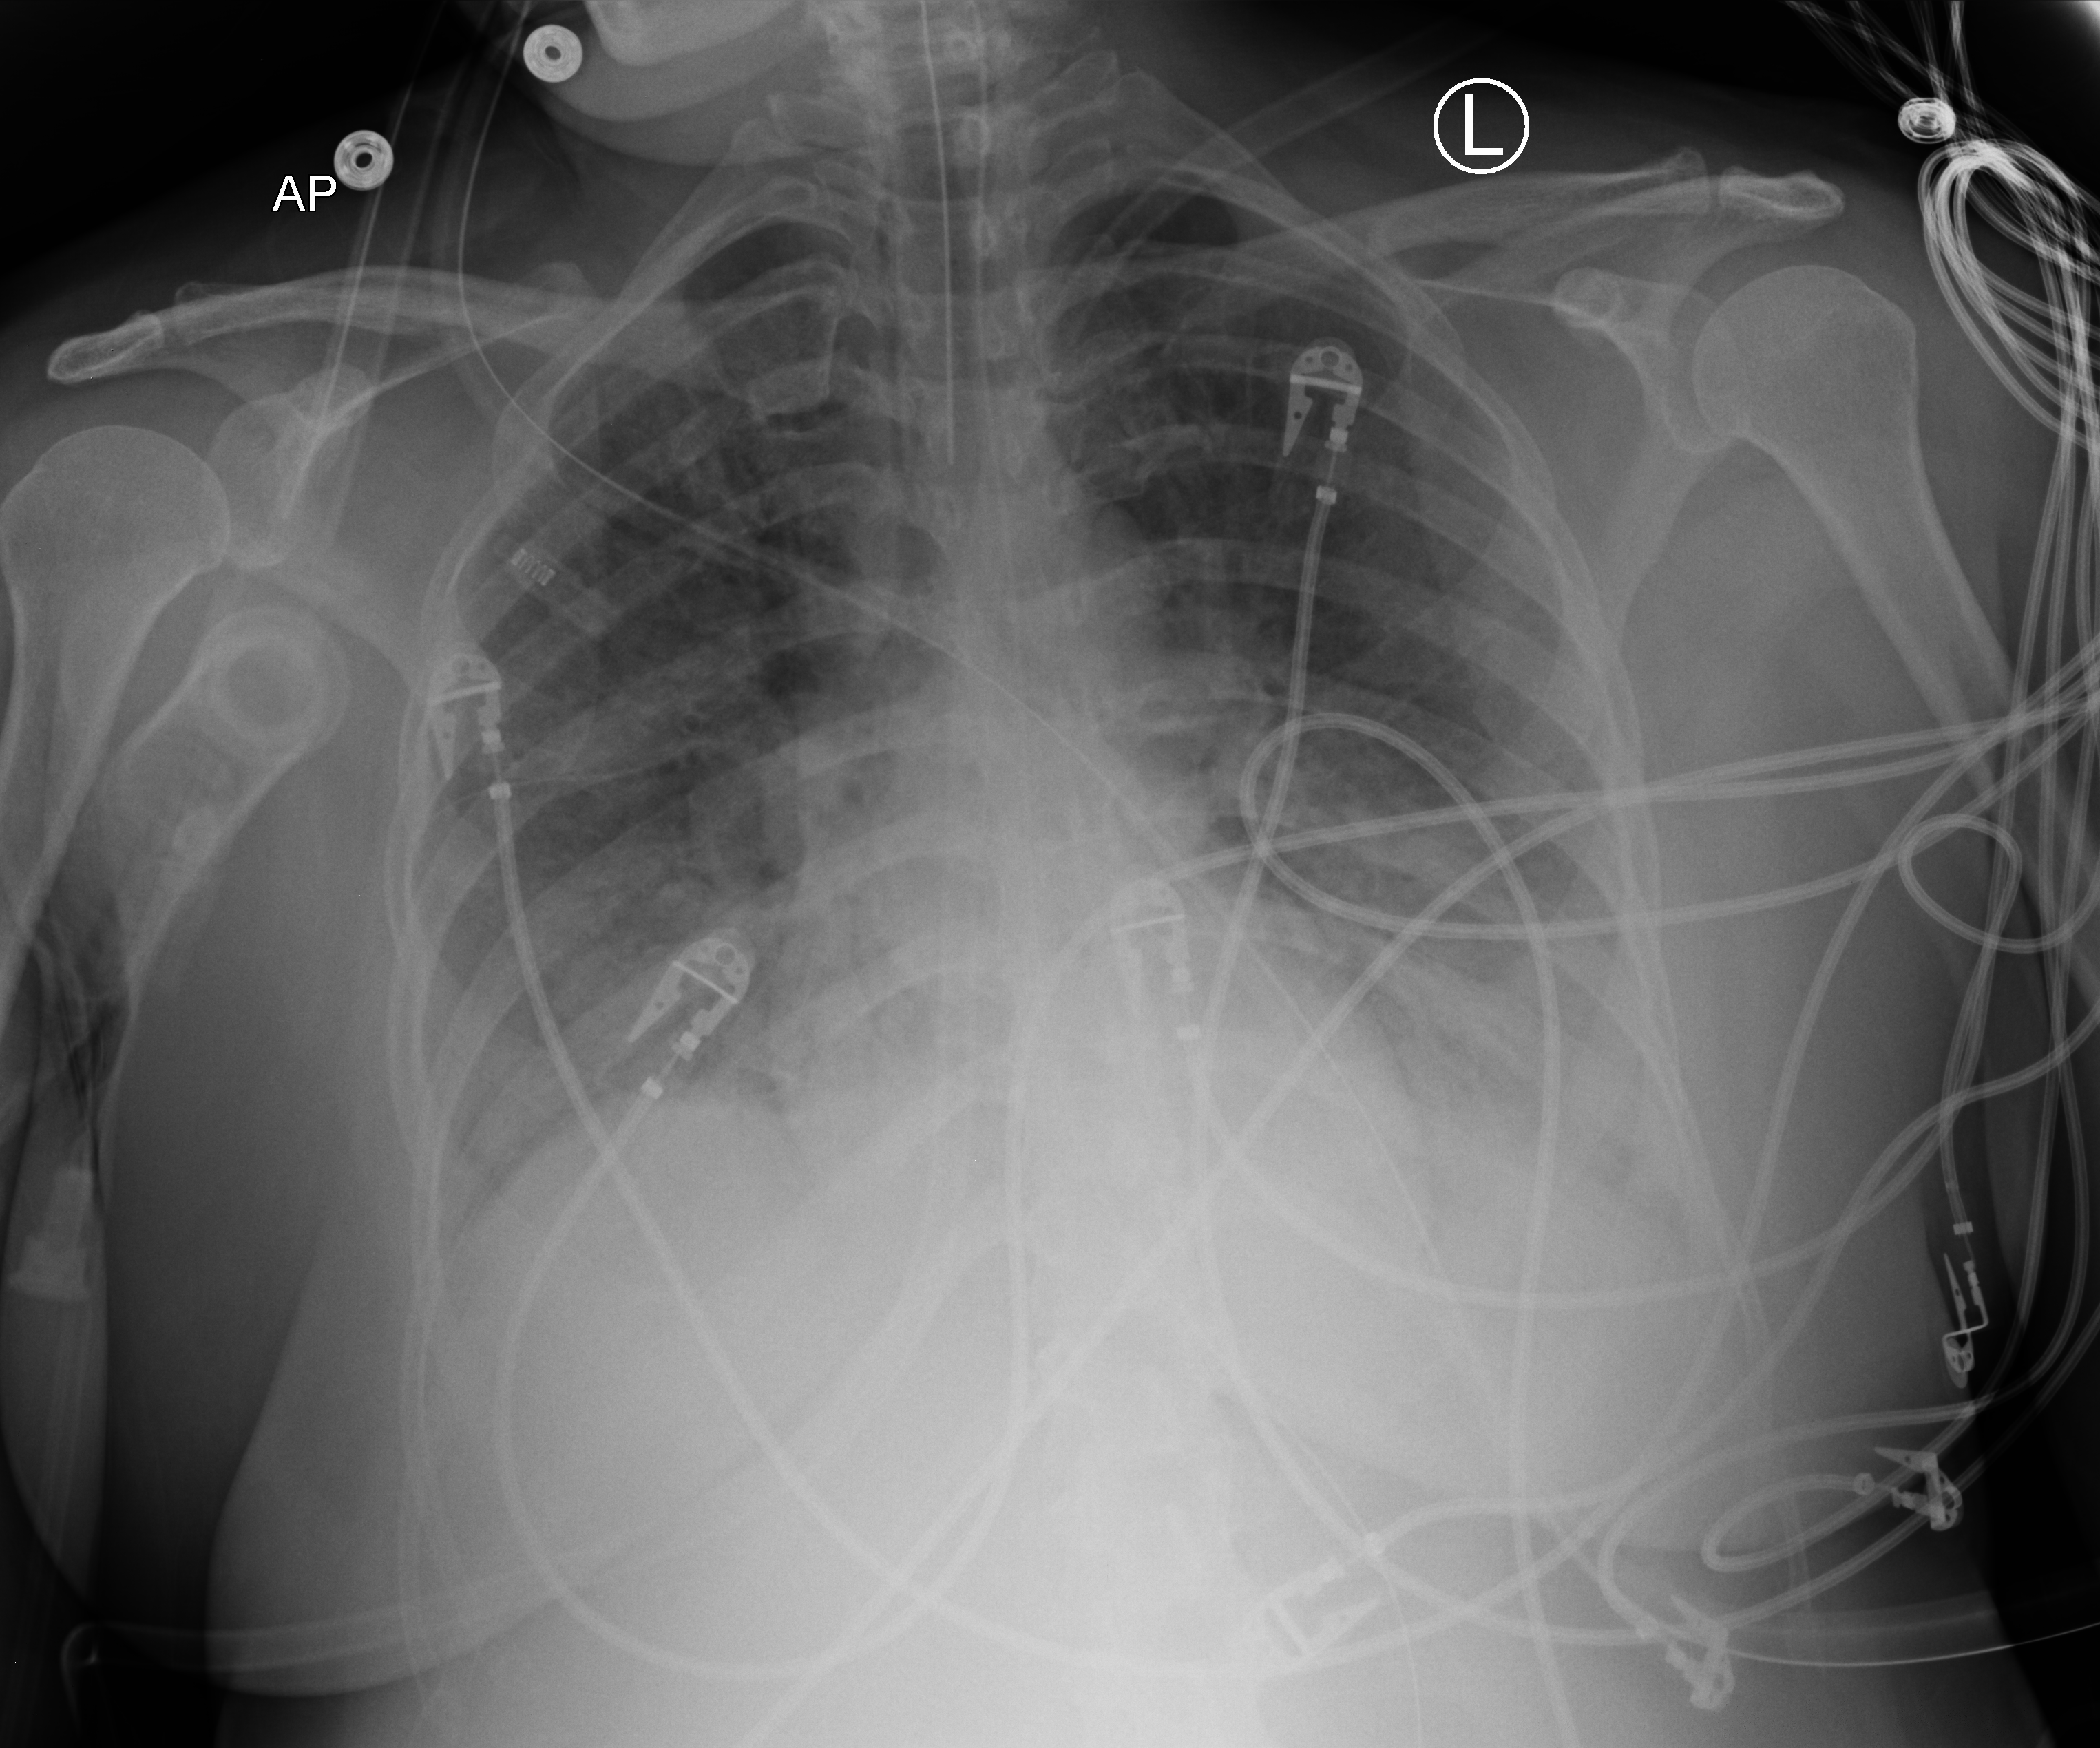
Bedside chest radiograph (computed radiography), anteroposterior (AP) projection. Male patient hospitalised with COVID-19, age 18–59 years.
Admission-level facts for this patient (not findings on this image; timing relative to this image not recorded):
- hypertension (admission record): yes